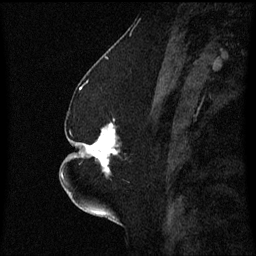
Breast MRI (dynamic contrast-enhanced), one sagittal slice; slice 25 of 60 in the series (ordered by position); dynamic contrast-enhanced series, image 2 of 3 at this slice position (ordered by acquisition); 1.5 T; TE 4.2 ms, TR 8.4 ms; 2.3 mm slice thickness; 256 × 256 image matrix, field of view 200 × 200 mm. Female patient, age 52 years. From the clinical record (not read from this slice): setting: breast cancer imaged before/during neoadjuvant chemotherapy; receptor status: HR-positive, HER2-negative.
Annotated regions visible in this slice (semi-automatically segmented with operator editing):
- analysis volume of interest (the breast-tissue region the enhancement analysis was run in; not a lesion): bounding box <75,120,127,179> (left, top, right, bottom; pixels)
- tumour enhancement mask (voxels above the 70 % enhancement threshold inside the analysis volume of interest): <75,124,118,175>